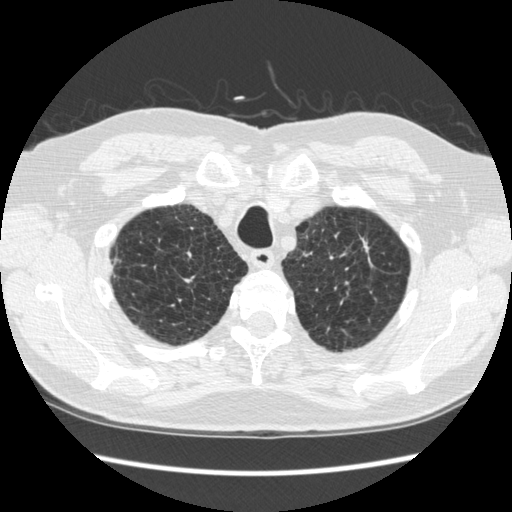
Chest CT (low-dose screening protocol), one axial image, second screening round (one year after baseline), lung window (W 1500 / L -600 HU), standard (soft-tissue) reconstruction kernel (STANDARD), 120 kVp, slice 44 of 295 in the series, 512 × 512 image matrix. Male, age 70 years at enrolment. Former smoker at enrolment.
- Expert-annotated lung lesion, bounding box <330,221,391,289> (left, top, right, bottom; pixels).
- The screening reader recorded 5 non-calcified nodules or masses ≥4 mm on this exam (right lower lobe, right lower lobe, right lower lobe, left upper lobe, left lower lobe); which of them this box marks is not recorded.
- Official screen result: positive, change unspecified: nodule(s) >= 4 mm or enlarging nodule(s), mass(es), or other non-specific abnormalities suspicious for lung cancer.